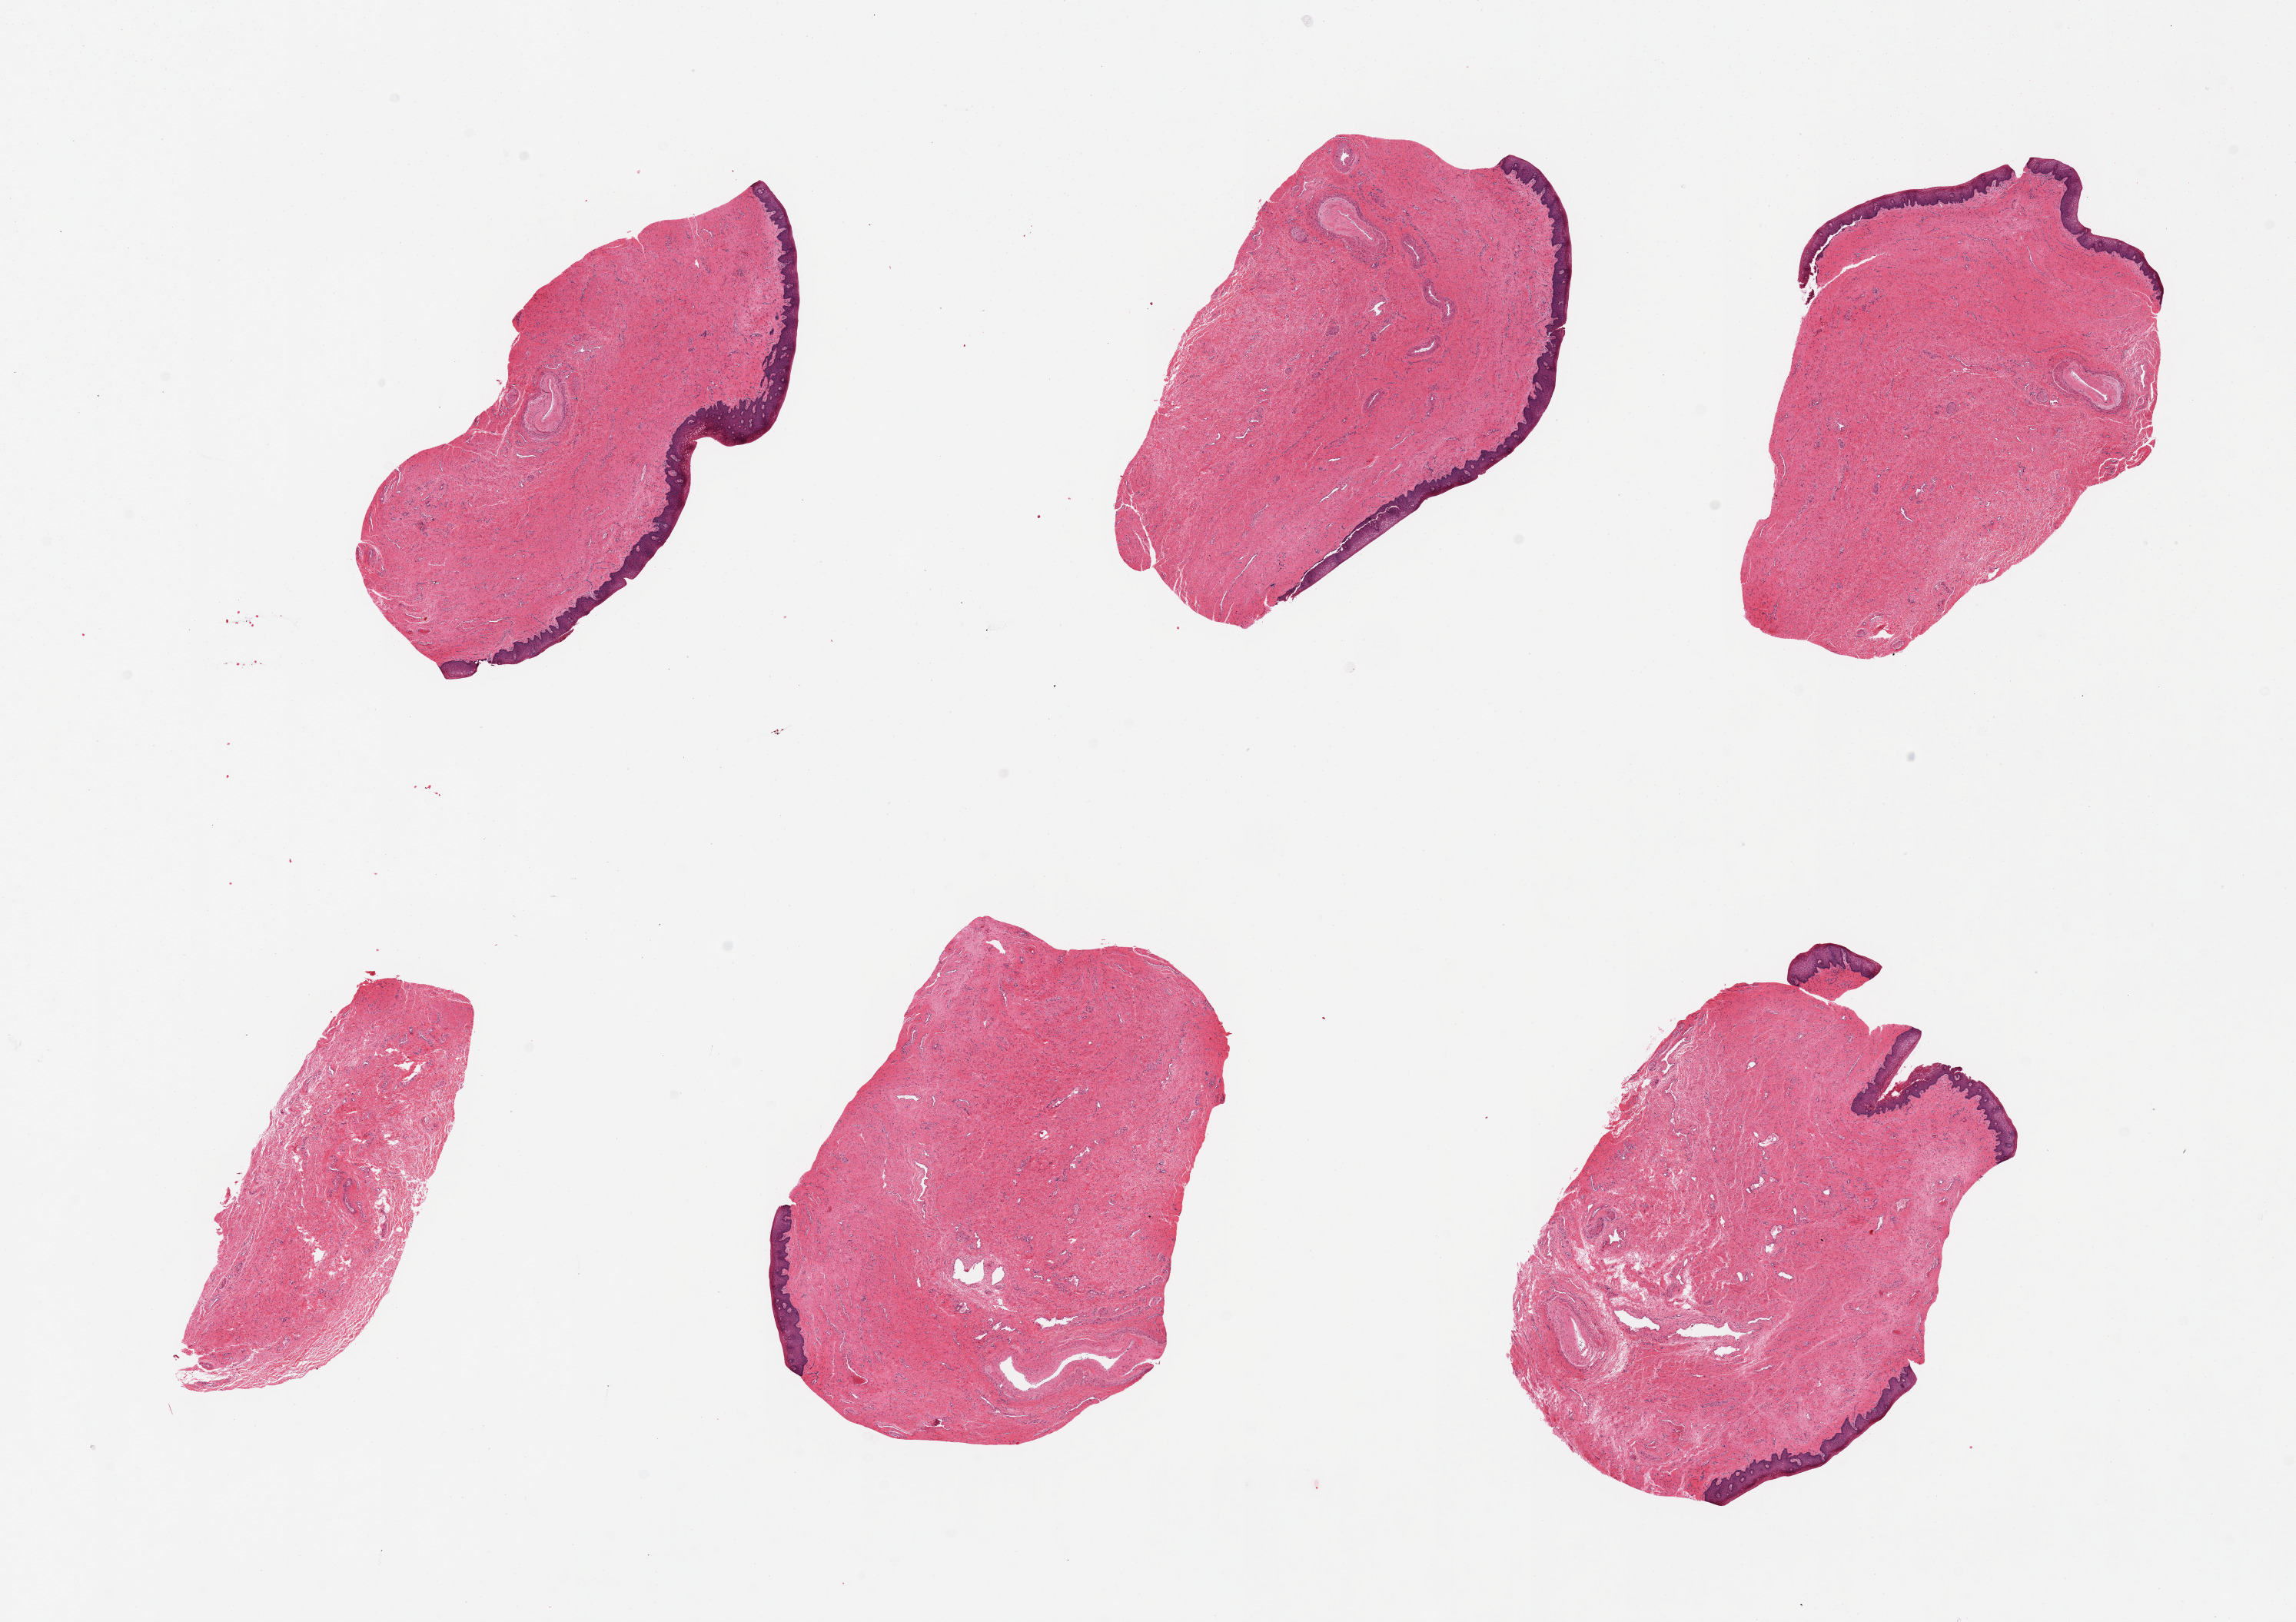
Whole-slide image, hematoxylin and eosin (H&E) stain — shown as a low-resolution overview of the whole scanned area (about 23.6 x 16.7 mm); PAXgene-fixed, paraffin-embedded tissue; sampled site (target tissue): vagina; donor tissue sample. Donor sex: female.
Reviewer comment on this tissue sample: 6 pieces.